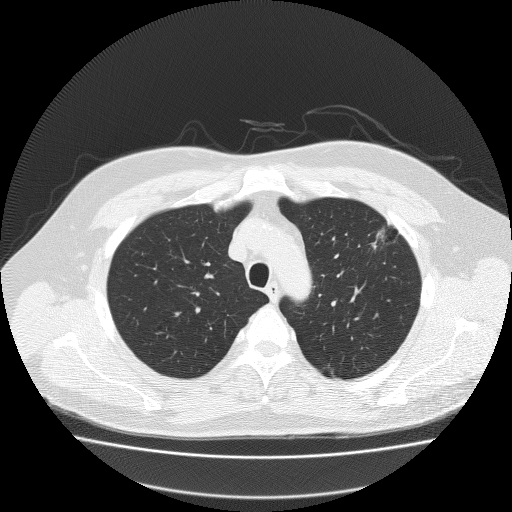
Low-dose screening chest CT, one axial slice; slice 159 of 204 in the series (ordered by position); reconstruction kernel FC51; lung window (W 1500 / L -600 HU); 2 mm slice thickness; 512 × 512 image matrix, field of view 410 × 410 mm.
Structures marked on this image (manually delineated by an expert):
- lesion 1 (tumor, upper lobe of left lung): bounding box <373,224,389,248> (left, top, right, bottom; pixels)